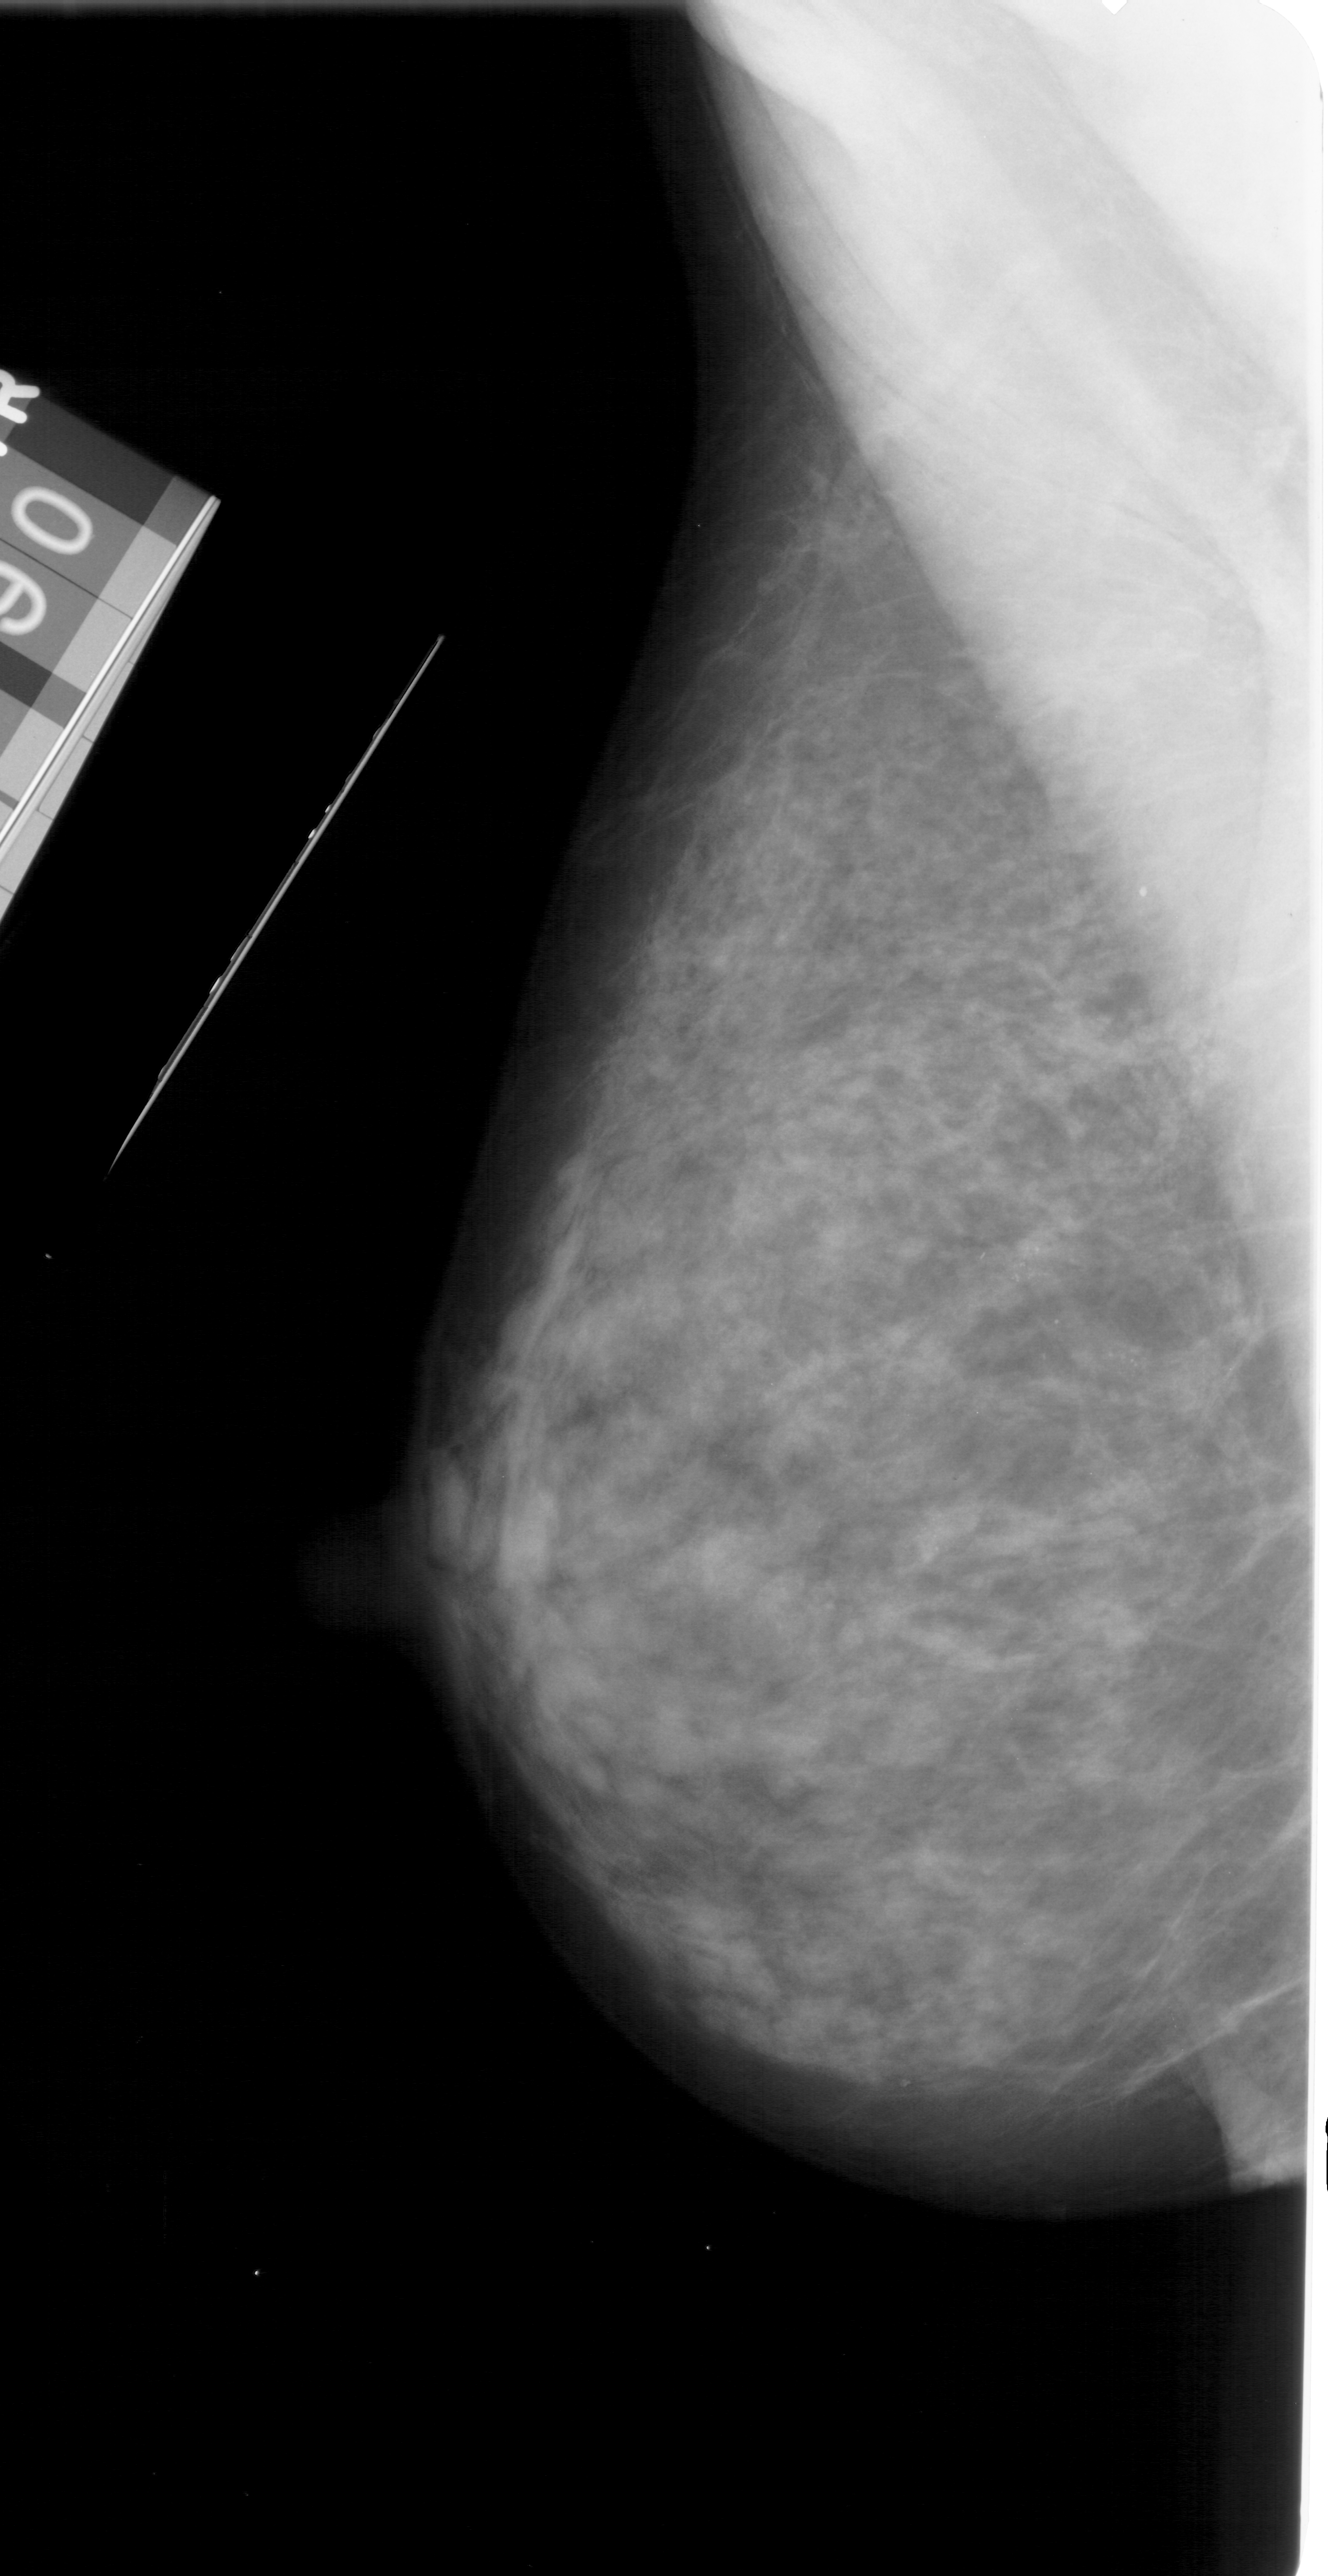
Mammogram (digitized film); left breast; MLO view; BI-RADS breast density category 3 (scale 1–4); 1328 × 2576 image matrix.
Expert-marked regions of interest on this film, with their recorded descriptors:
- calcifications, morphology pleomorphic, distribution segmental; BI-RADS assessment category 4; subtlety rating 3 on a 1 (subtle) to 5 (obvious) scale; pathology (as recorded): malignant: bounding box <825,1180,1239,1614> (left, top, right, bottom; pixels)